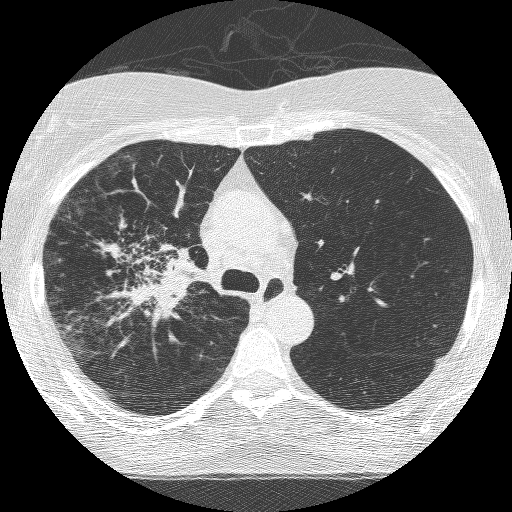
Axial slice from a low-dose chest CT screening exam. Third annual screen. Lung window (W 1500 / L -600 HU). 120 kVp. Slice 178 of 253 in the series. Female, age 64 years at enrolment. Former smoker at enrolment.
- Expert-annotated lung lesion, box from (x=92, y=225) to (x=206, y=338) px.
- Reader record for this screening exam (exam-level; its link to the box is not recorded): non-calcified nodule or mass ≥4 mm, right upper lobe, 49 × 43 mm, spiculated (stellate) margins, soft tissue attenuation, pre-existing on the prior screen: yes; interval growth: yes.